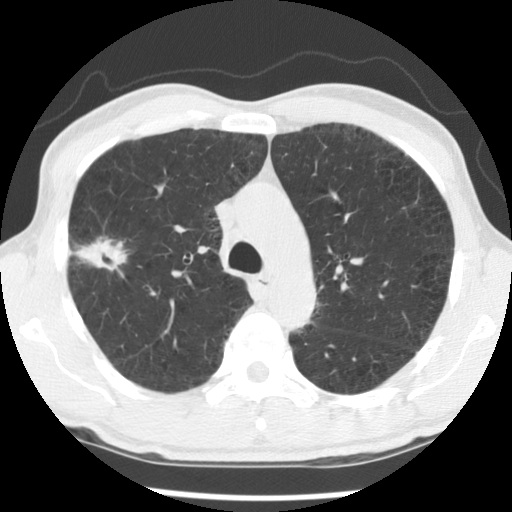
Low-dose screening chest CT, axial slice, second annual screen, lung window (W 1500 / L -600 HU), 2.5 mm slice thickness. Male participant, aged 56 years at enrolment.
Expert reader's lesion annotation, bounding box (x1, y1, x2, y2) in pixels: (54, 231, 140, 295). Screening reader's record for this exam (one nodule recorded; not confirmed to be the boxed lesion): non-calcified nodule or mass ≥4 mm, right upper lobe, 30 × 18 mm, spiculated (stellate) margins, mixed attenuation, pre-existing on the prior screen: yes; interval growth: yes. Later outcome: lung cancer diagnosed 326 days after this screen — squamous cell carcinoma, NOS, right upper lobe, right middle lobe, moderately differentiated (G2), stage IB (AJCC 6th edition), 70 mm at pathology.